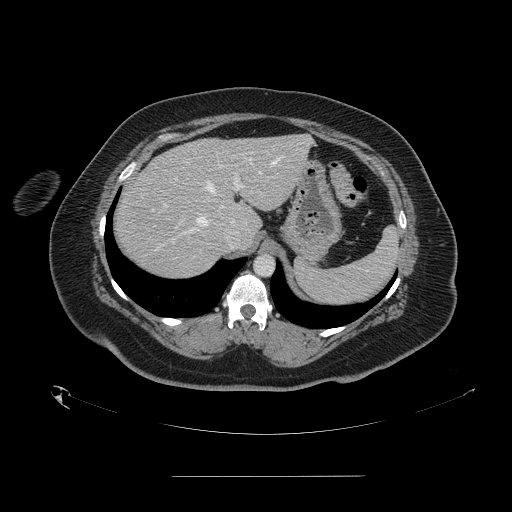
Contrast-enhanced abdominal CT, one axial slice. Position 115 of 164 along the scan axis. Intravenous contrast given. Soft-tissue window (W 400 / L 40 HU). 2.5 mm slice thickness. 512 × 512 image matrix, field of view 495 × 495 mm. Female patient, age 52 years. Case-level facts recorded for this patient, not image findings: diagnosis: colorectal cancer liver metastases, imaged before liver resection; multiple liver metastases: yes; largest metastasis: 3.5 cm; disease in both lobes: no.
Annotated regions visible in this slice (manually delineated by an expert):
- hepatic veins: bounding box <152,157,282,251> (left, top, right, bottom; pixels)
- liver: <114,135,312,279>
- planned liver remnant (the part of the liver to remain after resection): <170,136,312,226>
- portal vein (with intrahepatic branches): <164,177,242,208>